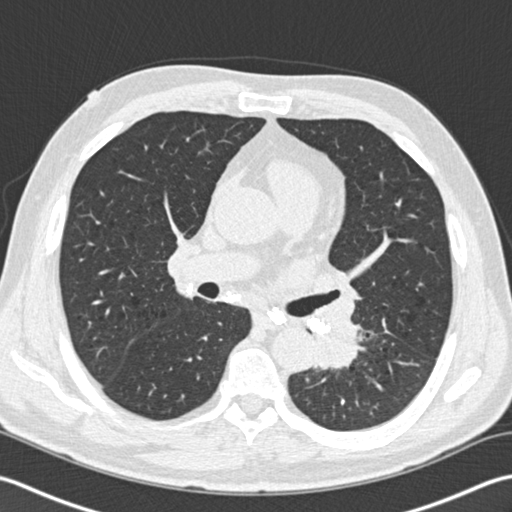
Low-dose screening chest CT, one axial slice. Reconstruction kernel B30f. 120 kVp. Lung window (W 1500 / L -600 HU). 2 mm slice thickness. 512 × 512 image matrix, field of view 350 × 350 mm.
Annotated regions visible in this slice (outlined manually by an expert reader):
- lesion 1 (tumor, lower lobe of left lung): bounding box [x1, y1, x2, y2] px = [315, 317, 361, 369]